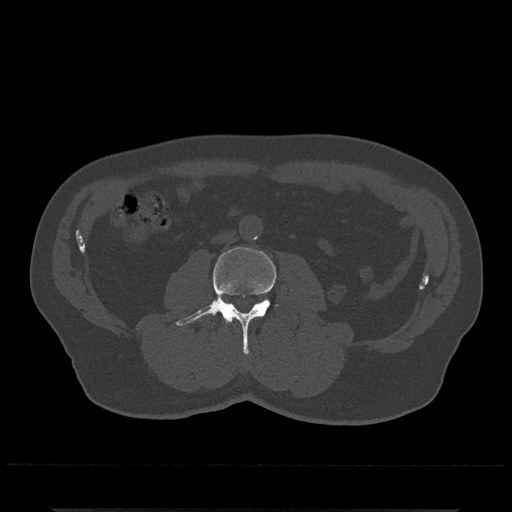
CT including the spine, one axial slice. Position 220 of 797 along the scan axis. Reconstruction kernel Br40s/3. 120 kVp. Bone window (W 1800 / L 400 HU). 0.5 mm slice thickness. 512 × 512 image matrix, field of view 393 × 393 mm. Male patient, age 67 years. From the clinical record (not read from this slice): primary cancer: prostate.
Outlined on this slice (semi-automatic segmentation, software-assisted and operator-edited):
- L3 vertebra: bounding box (x1, y1, x2, y2) in pixels: (175, 247, 279, 355)